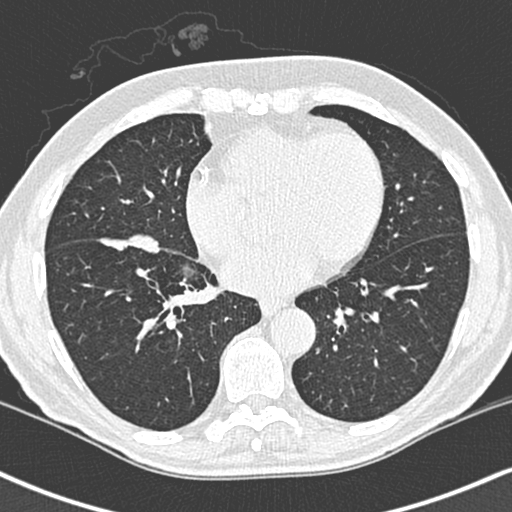
Low-dose screening chest CT, one axial slice; position 109 of 248 along the scan axis; 120 kVp; lung window (W 1500 / L -600 HU); 1.3 mm slice thickness; 512 × 512 image matrix, field of view 323 × 323 mm.
Structures marked on this image (manually delineated by an expert):
- lesion 1 (tumor, lower lobe of right lung): bounding box [x1, y1, x2, y2] px = [99, 197, 160, 215]